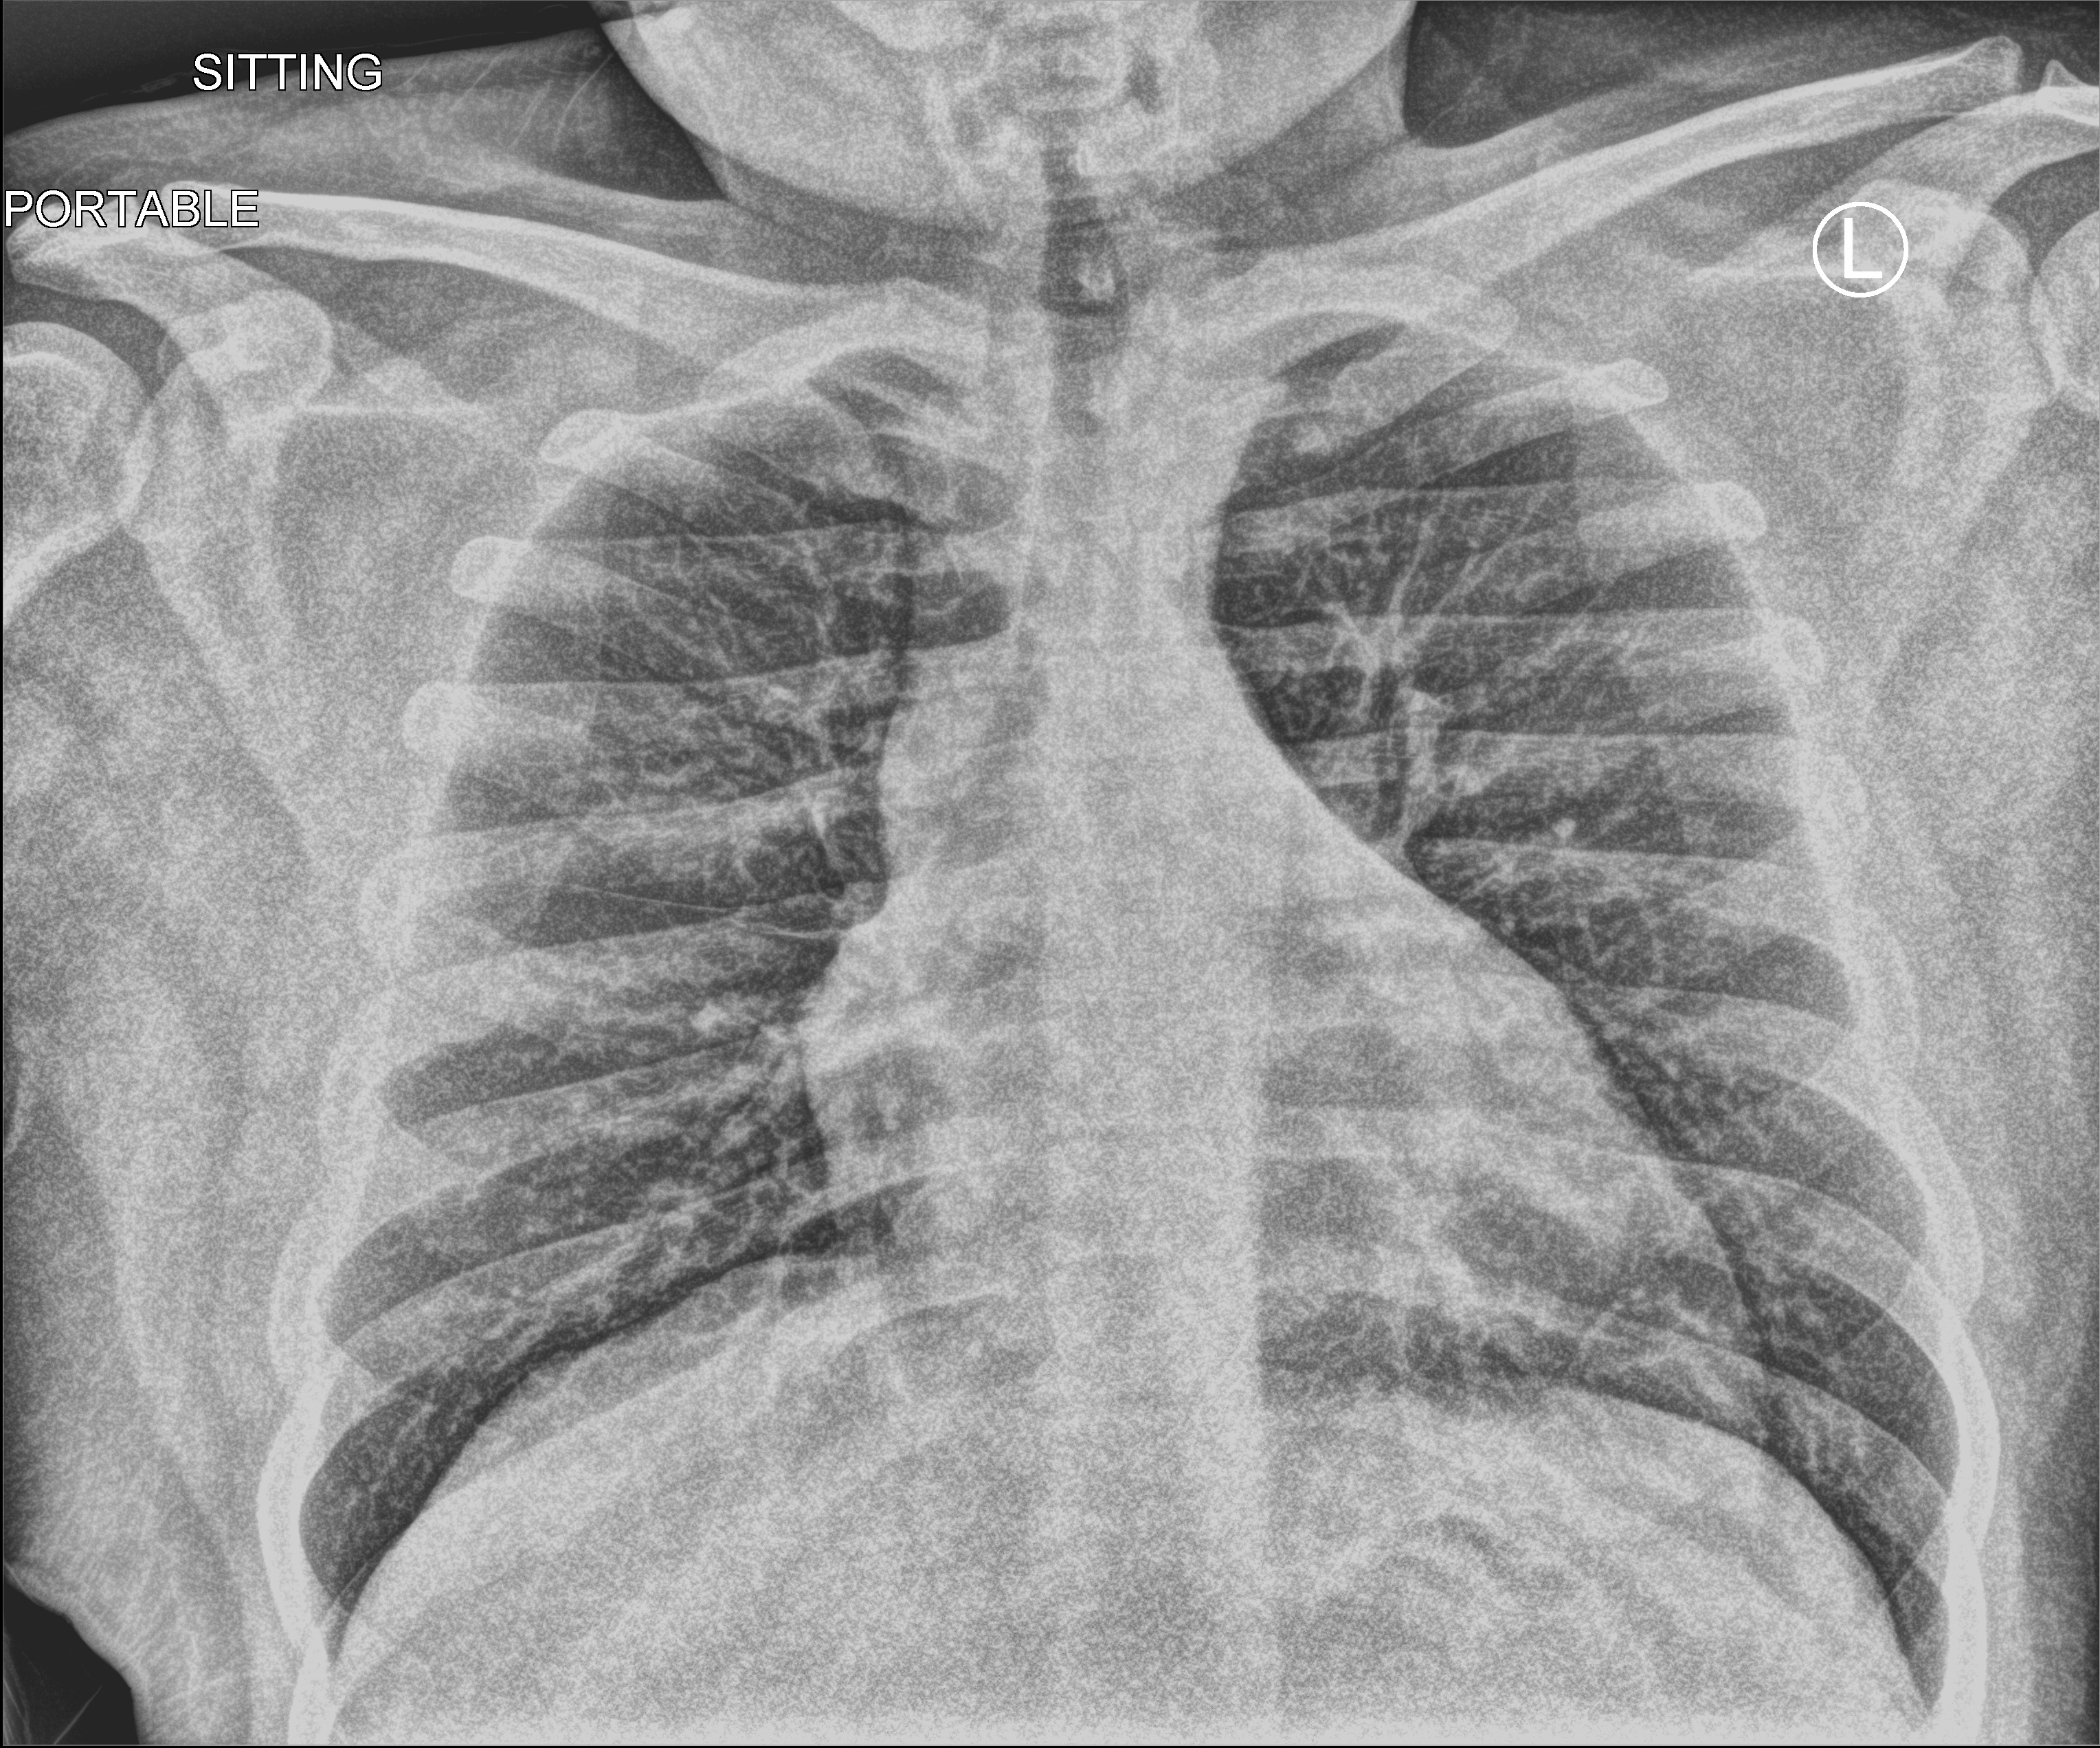
Bedside chest radiograph (computed radiography); anteroposterior (AP) projection. Female patient hospitalised with COVID-19, age 18–59 years.
Admission-level facts for this patient (not findings on this image; timing relative to this image not recorded):
- mechanically ventilated during this hospital stay: no
- length of hospital stay: 1 day